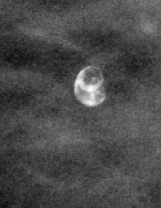
Region of interest cut from a scanned film mammogram (one marked finding), left breast, CC view.
Finding: calcifications, morphology vascular / coarse / lucent centered; BI-RADS assessment category 2; subtlety rating 5 on a 1 (subtle) to 5 (obvious) scale; benign without callback (not worked up further).